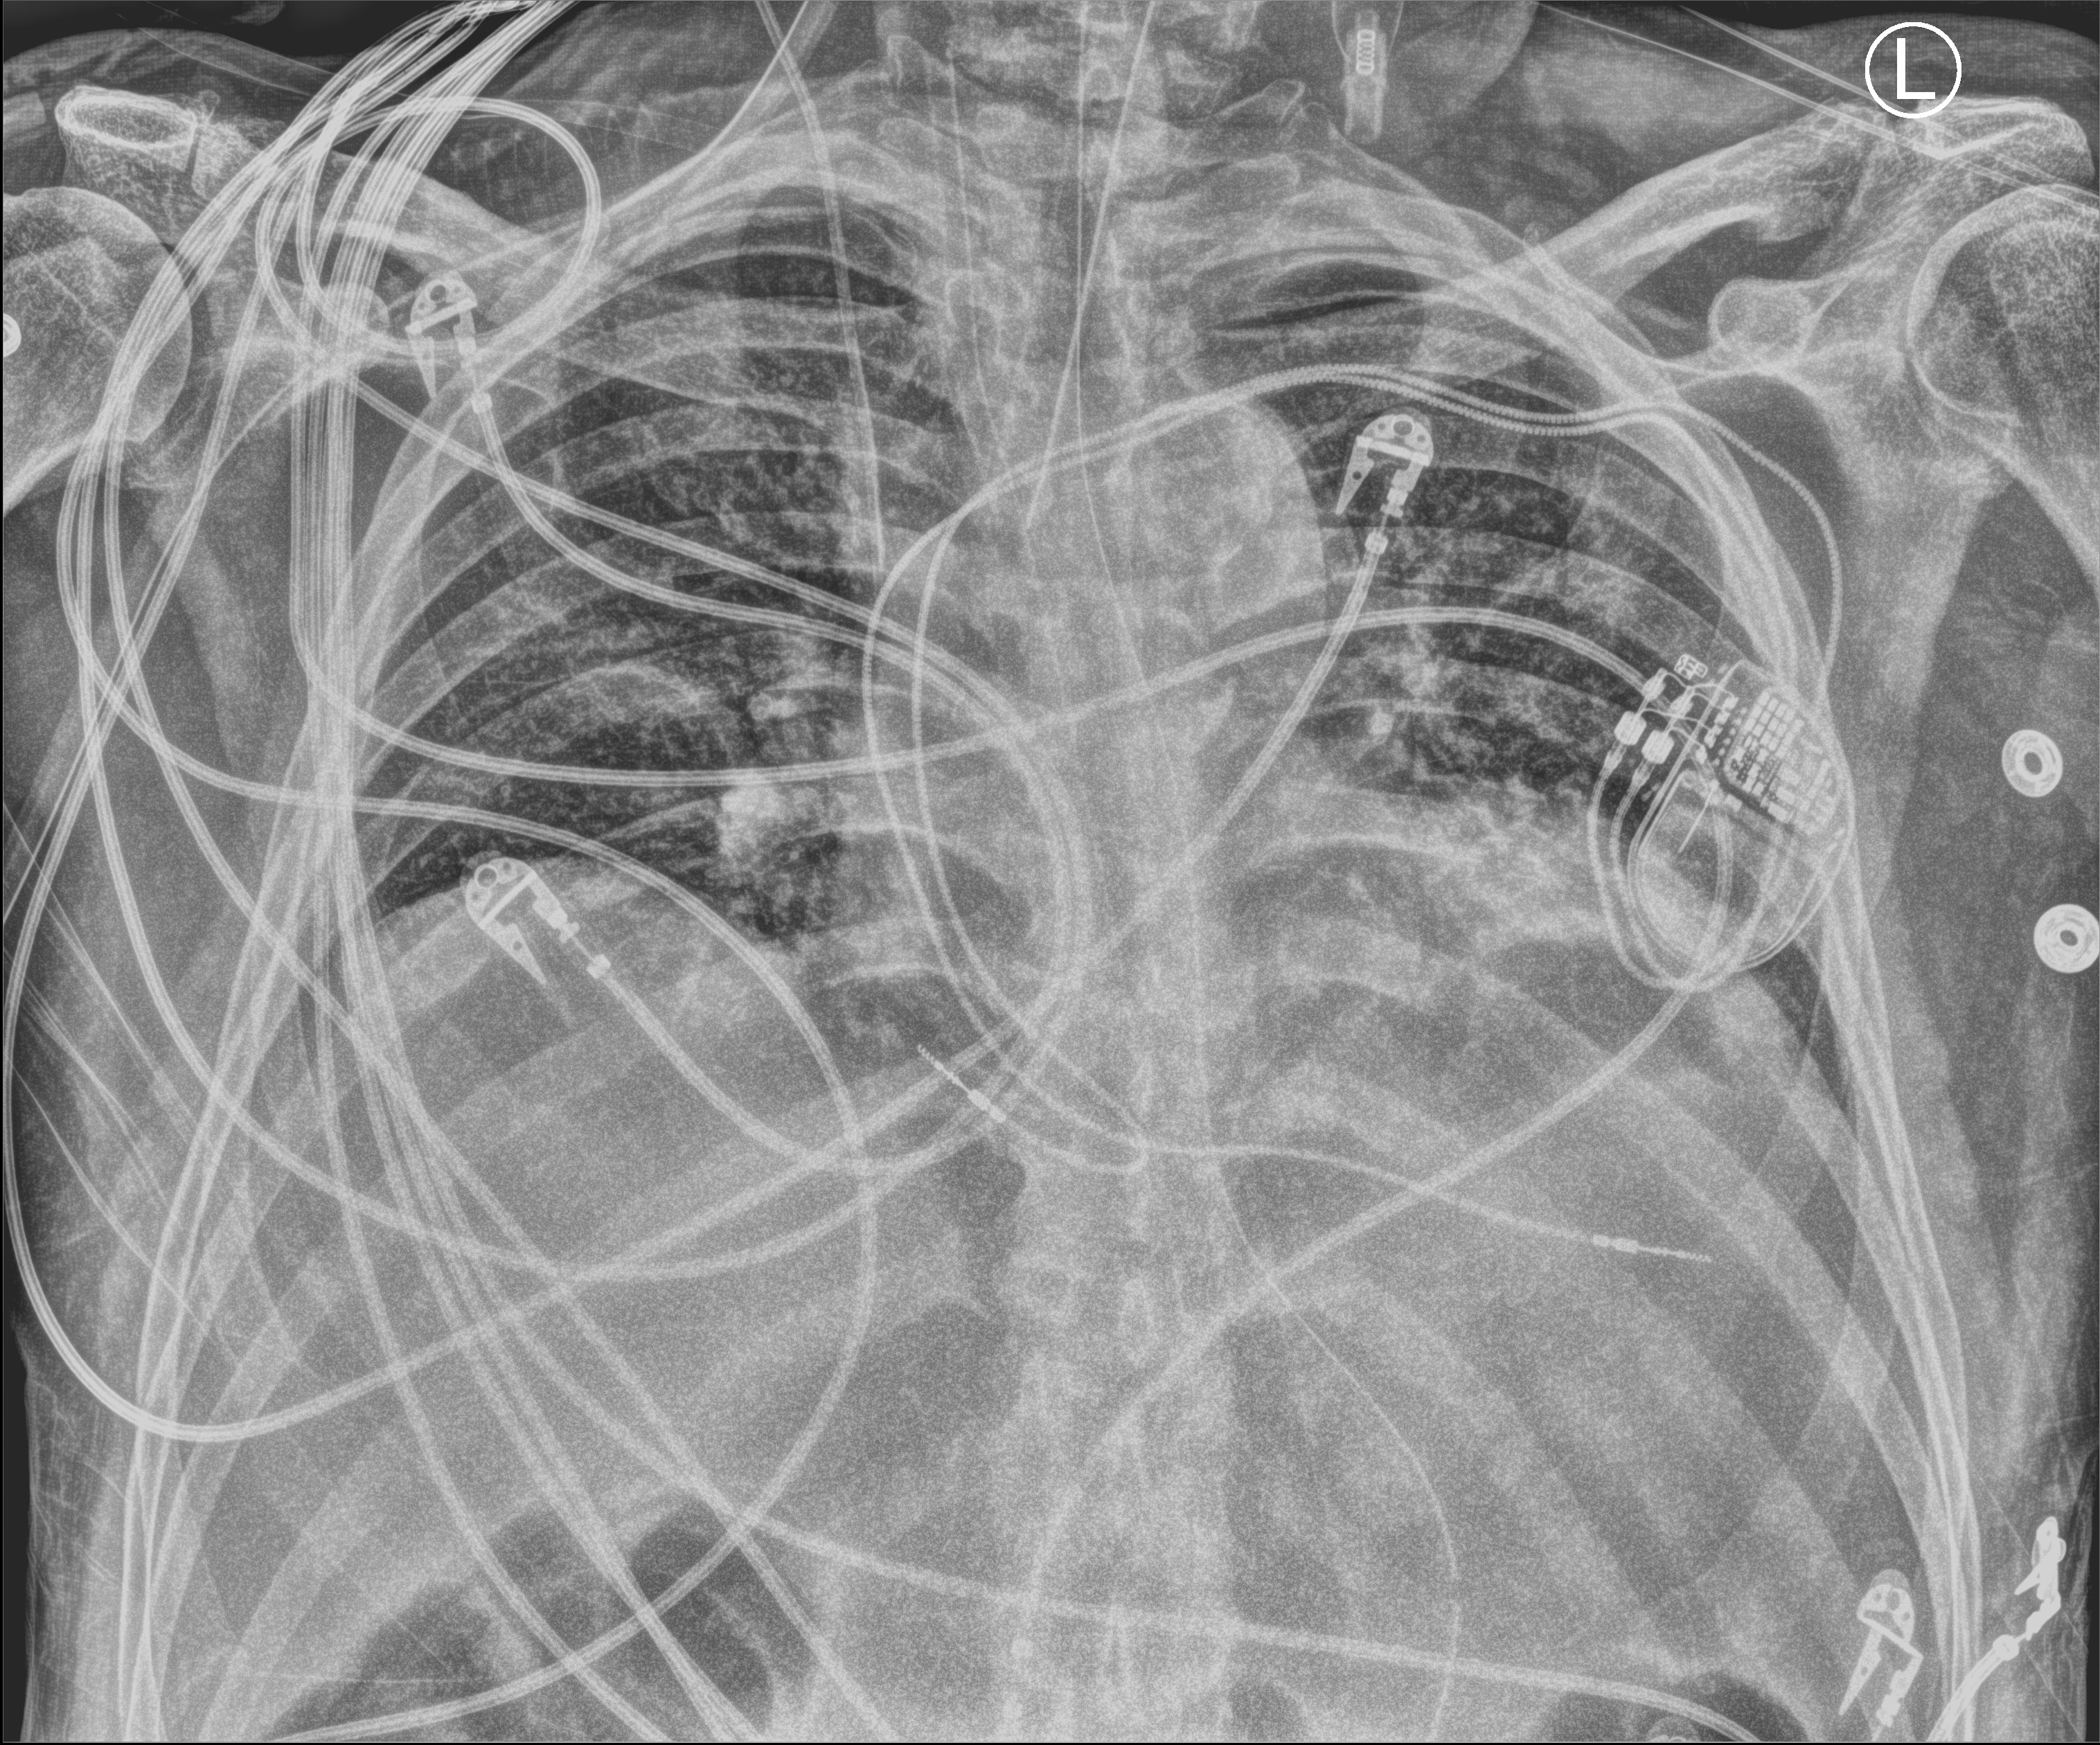
Portable chest radiograph, anteroposterior (AP) projection. Male patient hospitalised with COVID-19, age 60–74 years.
Hospital-stay facts (about this admission, not read from this image; timing relative to this image not recorded): admitted to intensive care during this hospital stay: yes.